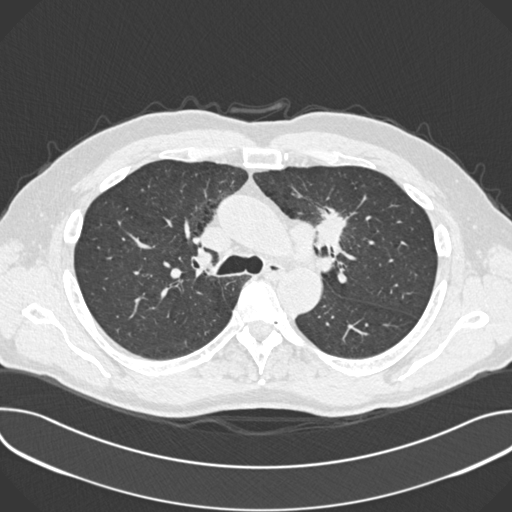
Low-dose screening chest CT, one axial slice; position 254 of 361 along the scan axis; reconstruction kernel B30f; 120 kVp; lung window (W 1500 / L -600 HU); 1 mm slice thickness; 512 × 512 image matrix.
Outlined on this slice (manually delineated by an expert):
- lesion 1 (tumor, upper lobe of left lung): box from (x=316, y=208) to (x=347, y=248) px